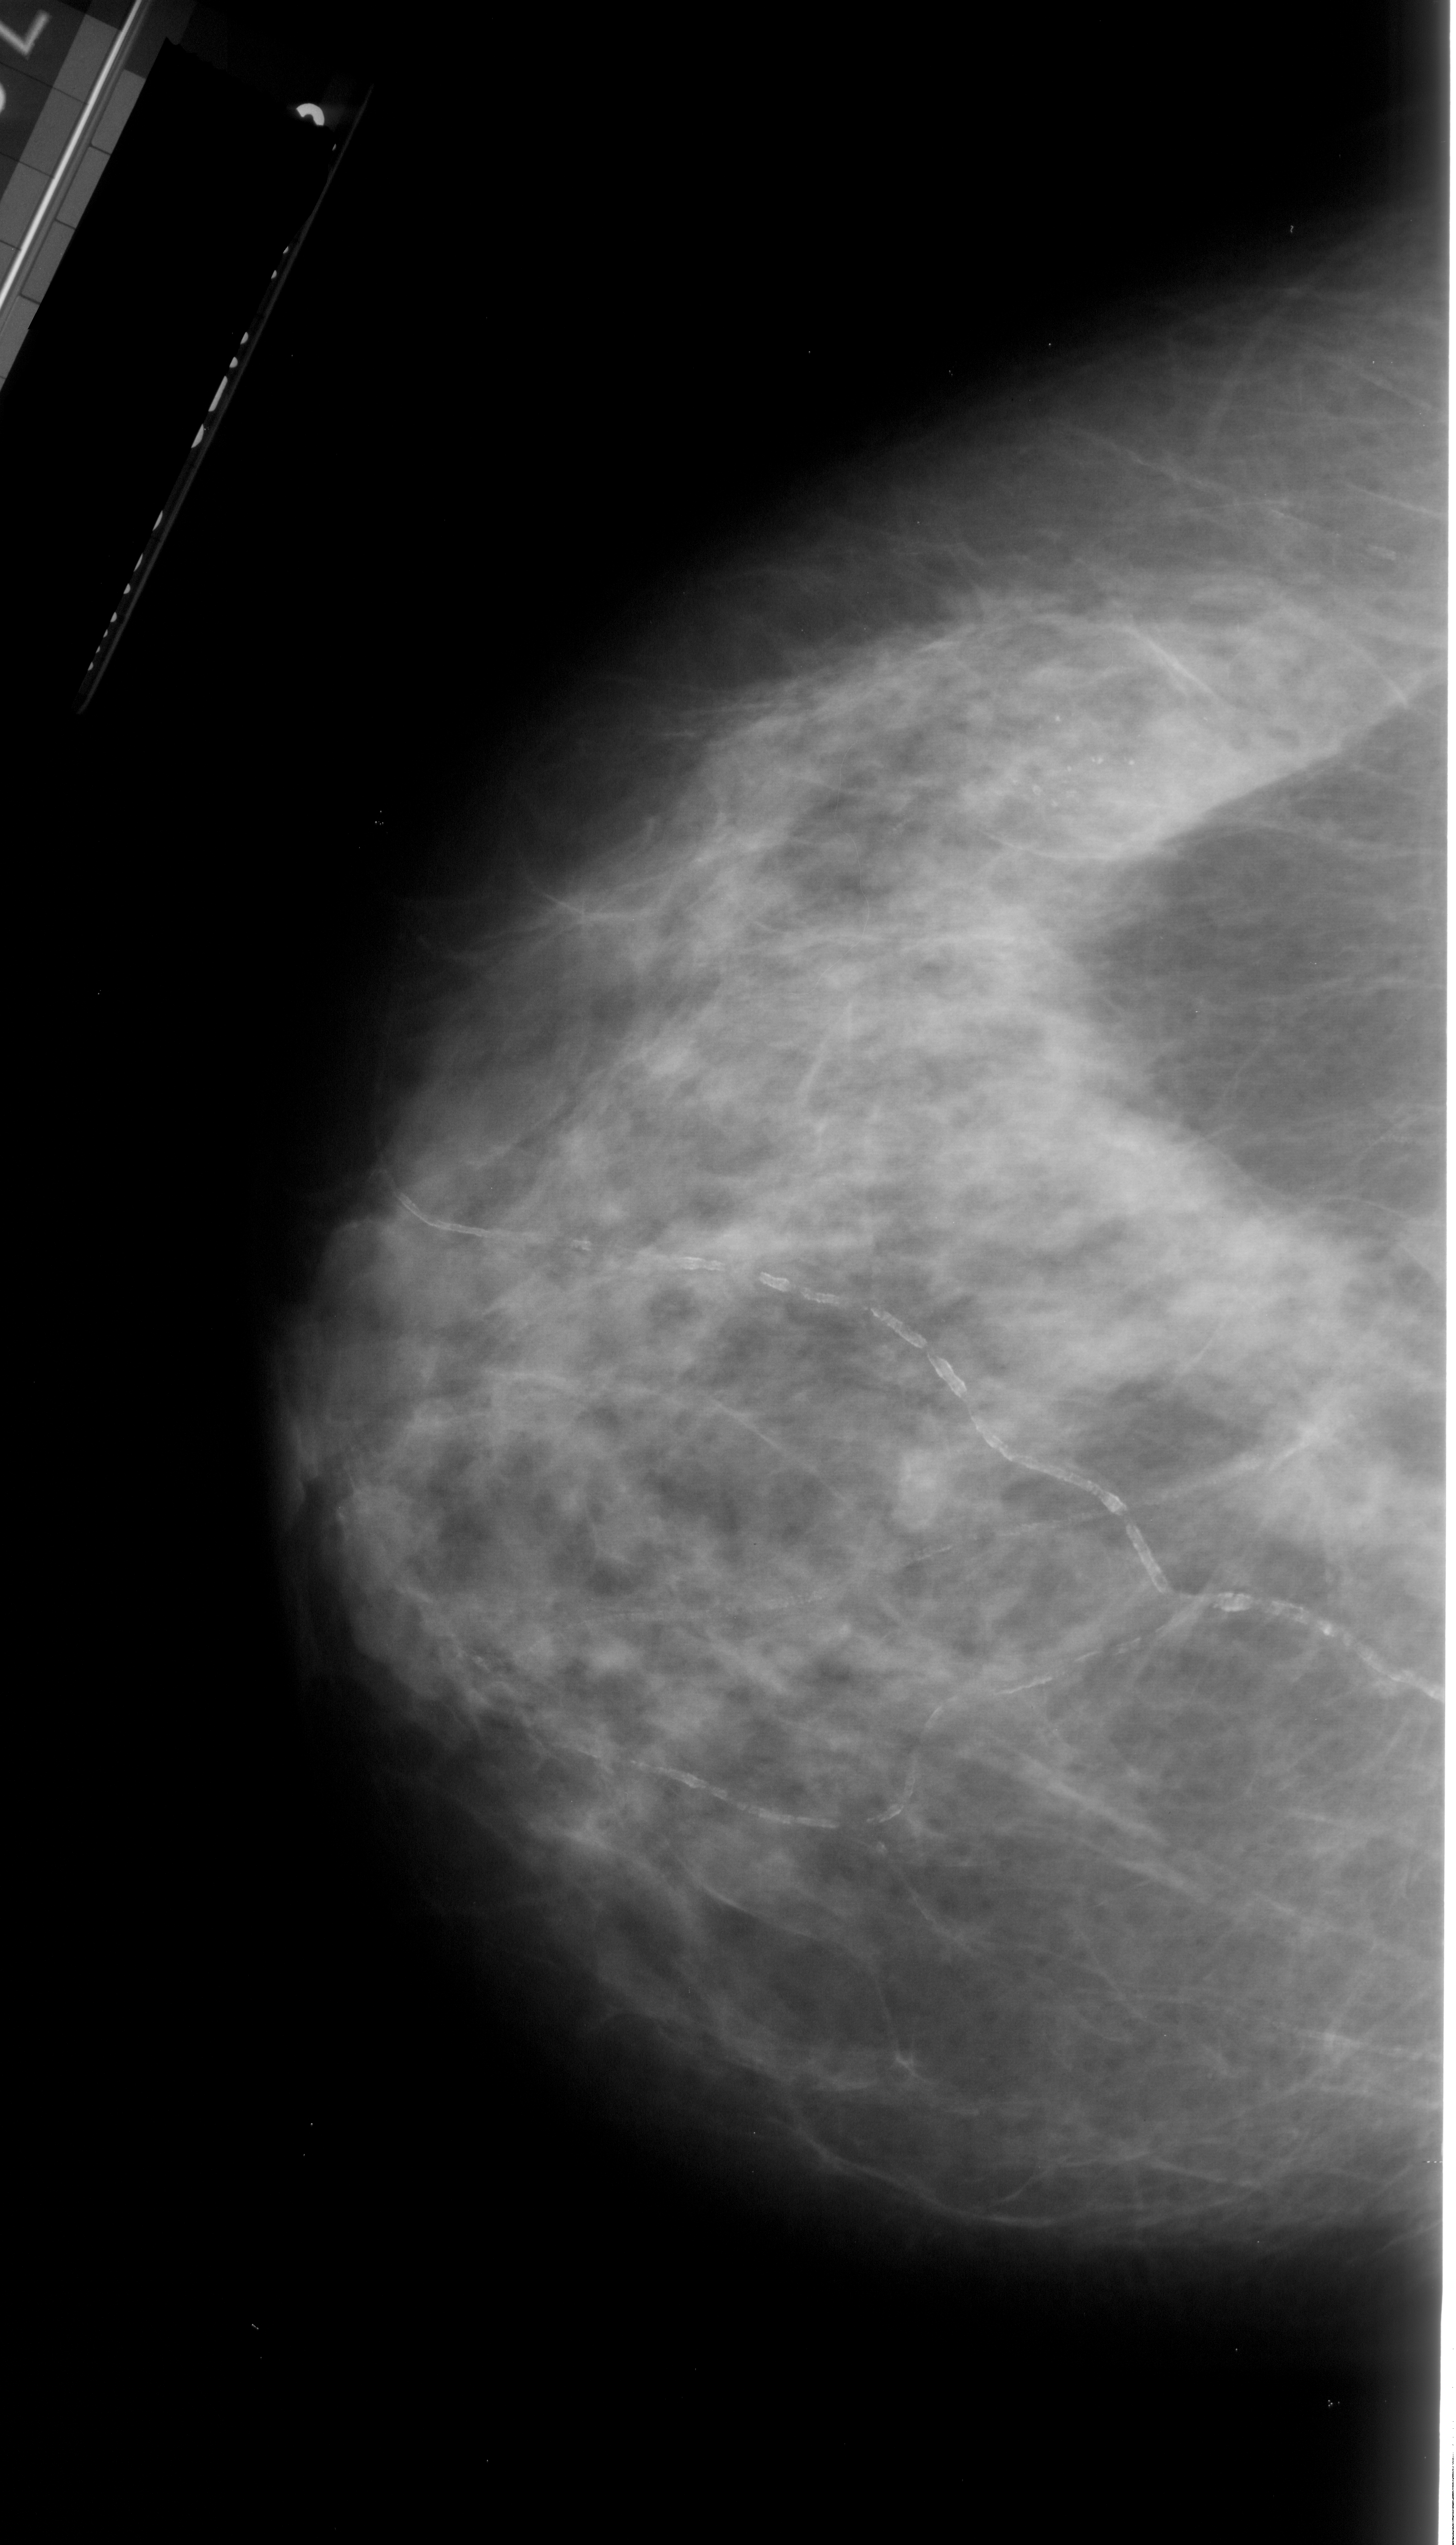
Scanned film-screen mammogram. Left breast. CC view. Breast composition: heterogeneously dense (BI-RADS density category 3 of 4). 1456 × 2545 image matrix.
Expert-marked regions of interest on this film, with their recorded descriptors:
- calcifications, morphology pleomorphic, distribution linear; BI-RADS assessment category 4; pathology result (as recorded, not read from the image): malignant: bounding box [x1, y1, x2, y2] px = [866, 698, 1175, 852]